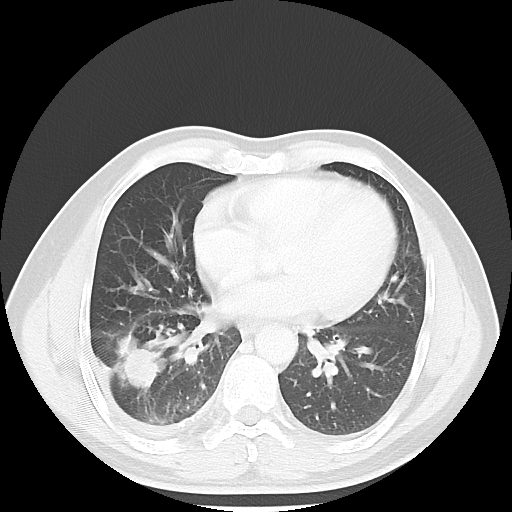
Chest CT, one axial slice. Position 23 of 56 along the scan axis. Reconstruction kernel LUNG. 120 kVp. Lung window (W 1500 / L -600 HU). 512 × 512 image matrix, field of view 344 × 344 mm. Male patient, age 56 years. From the clinical record (not read from this slice): clinical TNM (as recorded): T2 N3 M1.
Structures marked on this image (rectangle marked by the reading radiologist):
- lung tumour (recorded histology: adenocarcinoma): box from (x=114, y=333) to (x=167, y=398) px